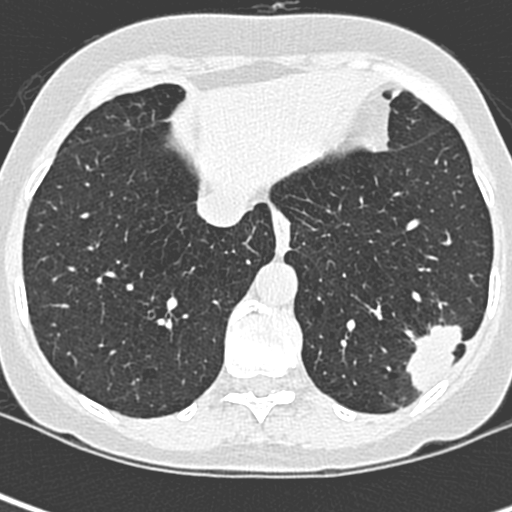
Low-dose screening chest CT, one axial slice; position 77 of 252 along the scan axis; lung window (W 1500 / L -600 HU); 1.3 mm slice thickness; 512 × 512 image matrix, field of view 271 × 271 mm.
Annotated regions visible in this slice (expert manual segmentation):
- lesion 1 (tumor, lower lobe of left lung): bounding box (x1, y1, x2, y2) in pixels: (406, 325, 465, 394)